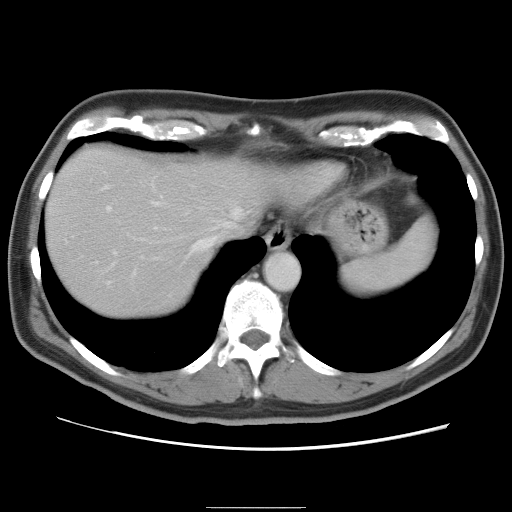
Contrast-enhanced abdominal CT, one axial slice. Position 70 of 87 along the scan axis. Intravenous contrast given. Soft-tissue window (W 400 / L 40 HU). 5 mm slice thickness. 512 × 512 image matrix, field of view 363 × 363 mm. Male patient, age 63 years. From the clinical record (not read from this slice): diagnosis: colorectal cancer liver metastases, imaged before liver resection; multiple liver metastases: no; largest metastasis: 9 cm; disease in both lobes: no.
Structures marked on this image (manually delineated by an expert):
- hepatic veins: bounding box <96,184,243,263> (left, top, right, bottom; pixels)
- liver: <45,148,268,319>
- planned liver remnant (the part of the liver to remain after resection): <45,167,215,318>
- portal vein (with intrahepatic branches): <105,204,159,284>